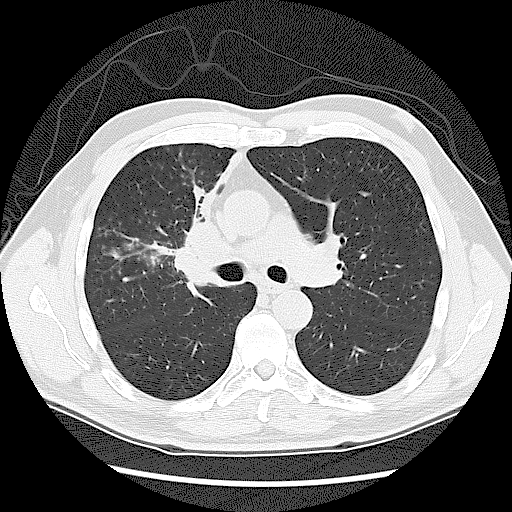
Low-dose screening chest CT, axial slice, first (baseline) screen, lung window (W 1500 / L -600 HU), 2.5 mm slice thickness, 120 kVp, 512 × 512 image matrix, field of view 360 × 360 mm. Male, age 60 years at enrolment. Current smoker at enrolment.
- Lesion marked by an expert reader, bounding box (x1, y1, x2, y2) in pixels: (158, 220, 242, 313).
- Screening reader's record for this exam: no non-calcified nodule ≥4 mm recorded.
- Lung cancer was diagnosed 41 days after this screen: small cell carcinoma, NOS, right upper lobe, stage IIIA (AJCC 6th edition).